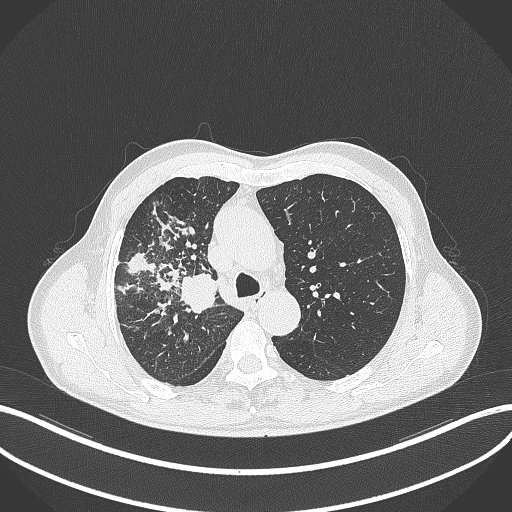
Chest CT, one axial slice; position 339 of 490 along the scan axis; 120 kVp; lung window (W 1500 / L -600 HU); 512 × 512 image matrix, field of view 400 × 400 mm. Patient: male, 69 years. From the clinical record (not read from this slice): clinical TNM (as recorded): T2a N0 M0.
Annotated regions visible in this slice (rectangle marked by the reading radiologist):
- lung tumour (recorded histology: adenocarcinoma): bounding box [x1, y1, x2, y2] px = [176, 269, 220, 315]